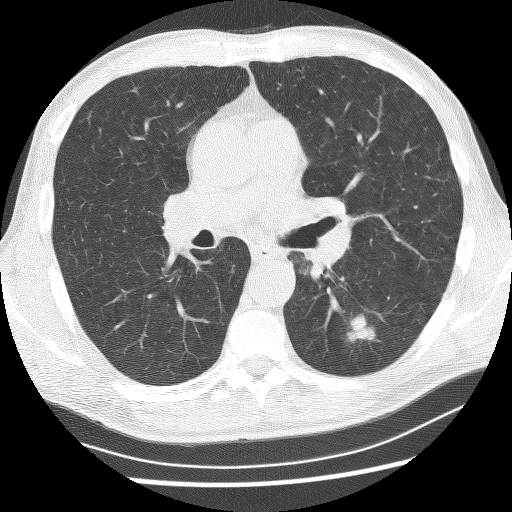
Axial slice from a low-dose chest CT screening exam; baseline annual screen; lung window (W 1500 / L -600 HU); 2.5 mm slice thickness; 120 kVp; slice 113 of 253 in the series; 512 × 512 image matrix, field of view 340 × 340 mm. Male participant, aged 62 years at enrolment. Current smoker at enrolment.
Lesion marked by an expert reader, bounding box [x1, y1, x2, y2] px = [329, 305, 384, 350]. Reader record for this screening exam (exam-level; its link to the box is not recorded): non-calcified nodule or mass ≥4 mm, left lower lobe, 21 × 17 mm, spiculated (stellate) margins, soft tissue attenuation. Official screen result: positive, change unspecified: nodule(s) >= 4 mm or enlarging nodule(s), mass(es), or other non-specific abnormalities suspicious for lung cancer. Later outcome: lung cancer diagnosed 58 days after this screen — non-small cell carcinoma, left lower lobe, poorly differentiated (G3), stage IA (AJCC 6th edition), 11 mm at pathology.